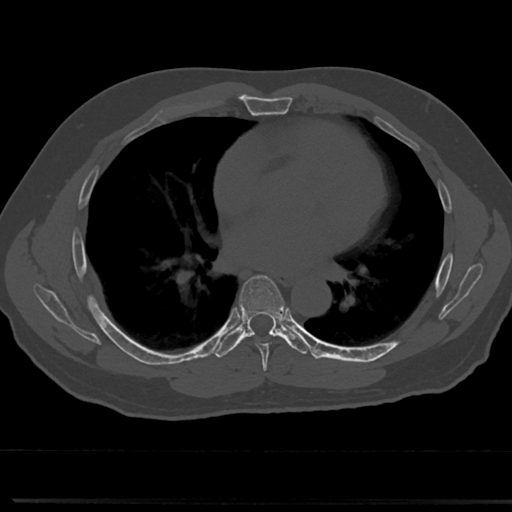
CT including the spine, one axial slice. Slice 422 of 817 in the series (ordered by position). Bone window (W 1800 / L 400 HU). 0.5 mm slice thickness. 512 × 512 image matrix. Patient: male, 61 years. From the clinical record (not read from this slice): primary cancer: prostate.
Annotated regions visible in this slice (semi-automatic segmentation, software-assisted and operator-edited):
- T6 vertebra: bounding box (x1, y1, x2, y2) in pixels: (240, 275, 287, 360)
- T7 vertebra: (239, 315, 286, 335)